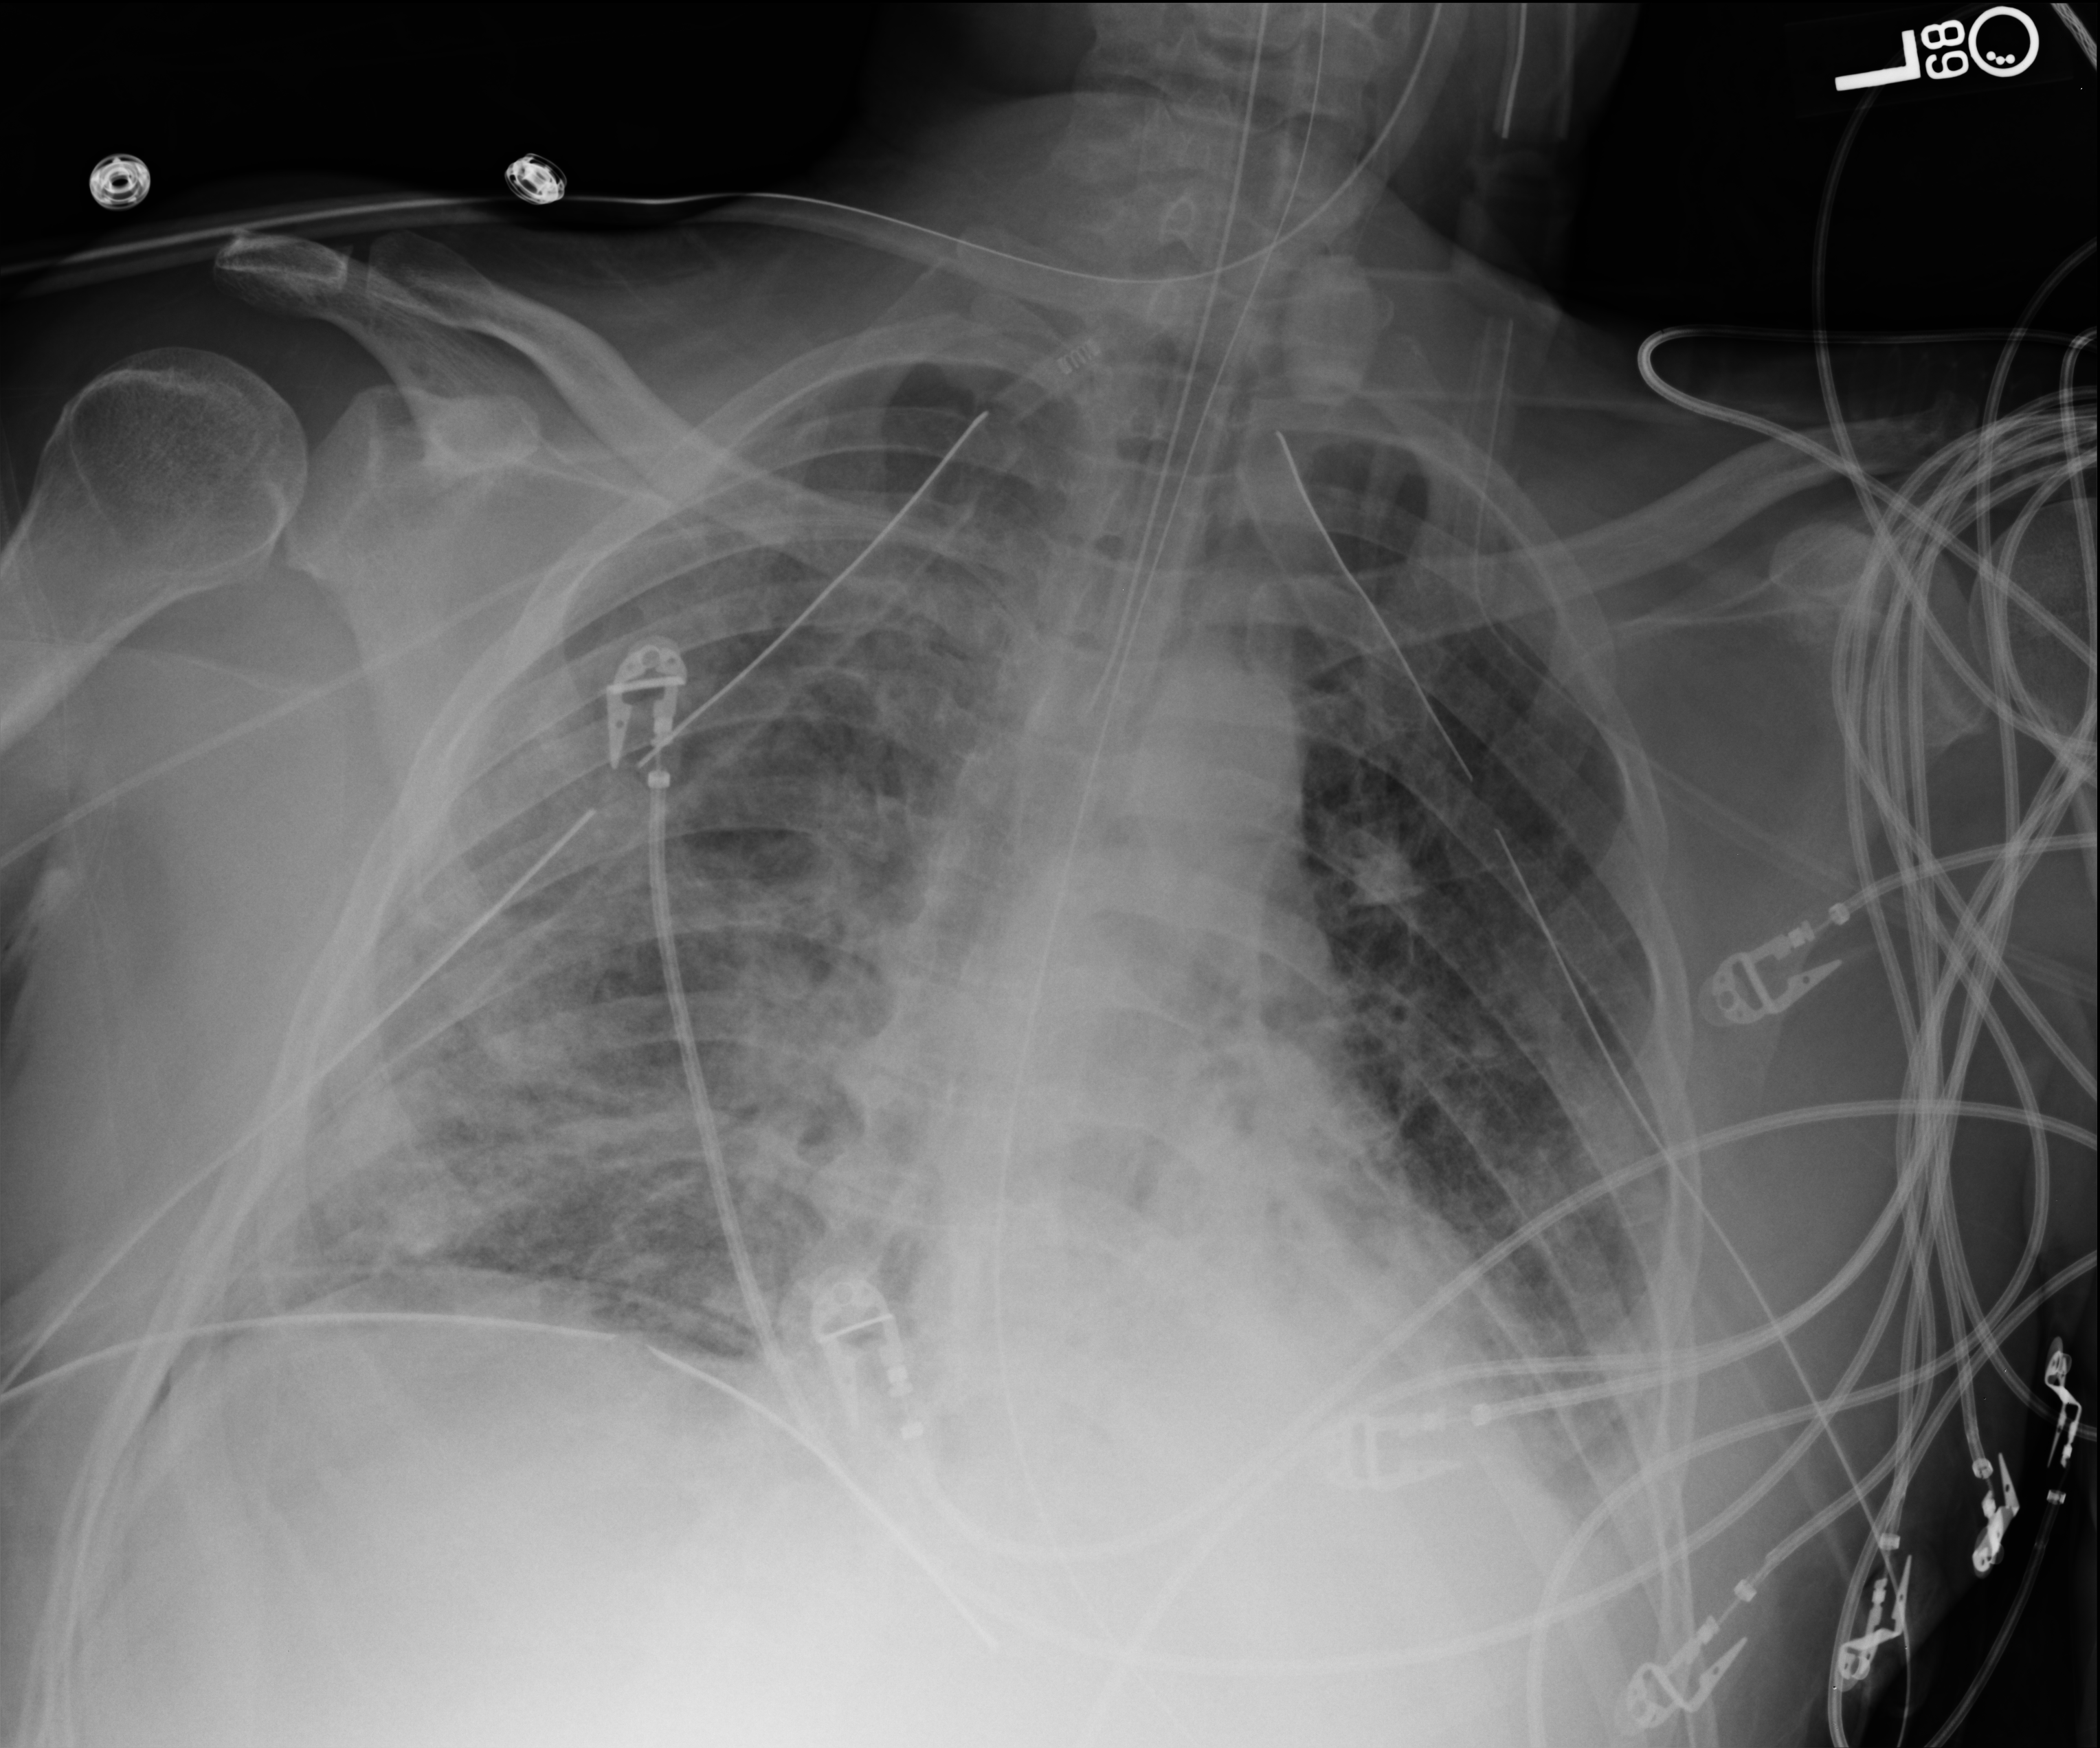
Bedside chest radiograph (computed radiography); anteroposterior (AP) projection. Patient hospitalised with COVID-19; male, aged 18–59 years.
From the hospital-stay record, not from the radiograph (when in the stay this image was taken is not recorded): mechanically ventilated during this hospital stay: yes.